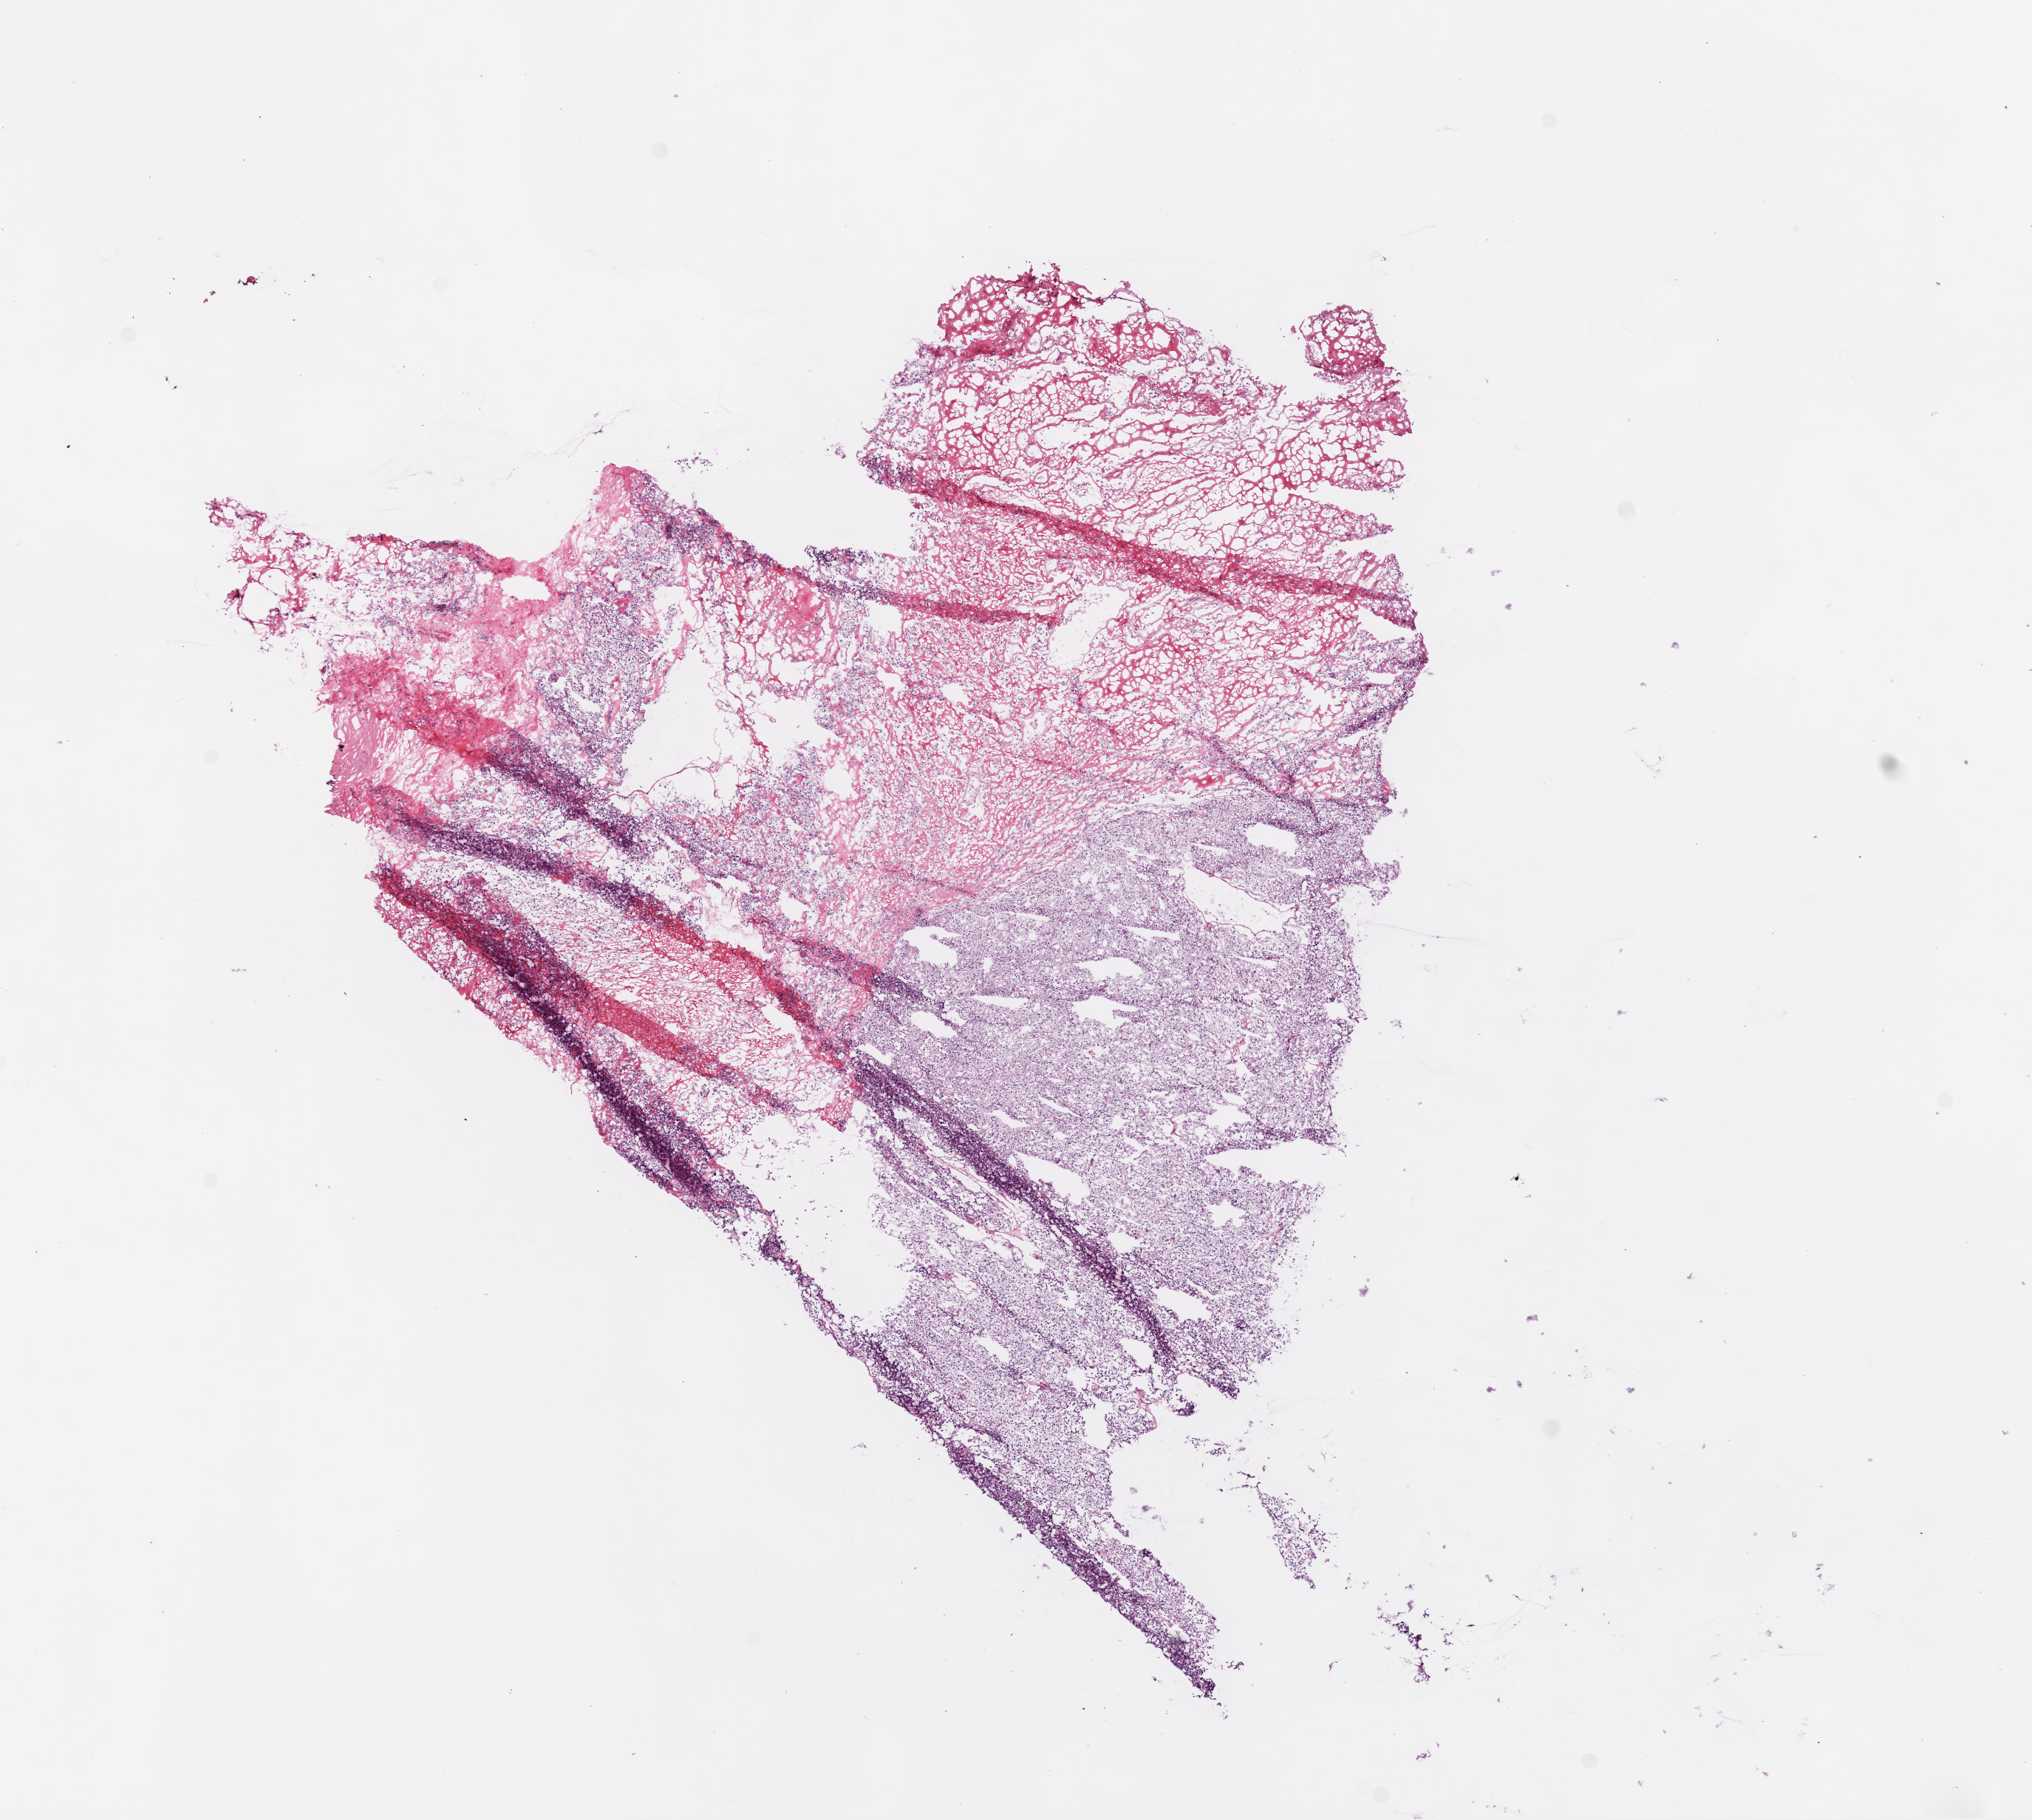
H&E-stained whole-slide image, low-resolution overview of the scanned area, about 11.0 x 9.9 mm (acquisition: 20x scan), frozen section, kidney, primary tumour sample. Patient: male, age at initial diagnosis 69 years. Histologic grade: G3 (poorly differentiated). Composition of this section per pathologist review: tumour cells 70%, tumour nuclei 70%, normal cells 0%, stromal cells 10%, necrosis 20%.
- AJCC pathologic stage: I
- diagnosis: Clear cell adenocarcinoma, NOS